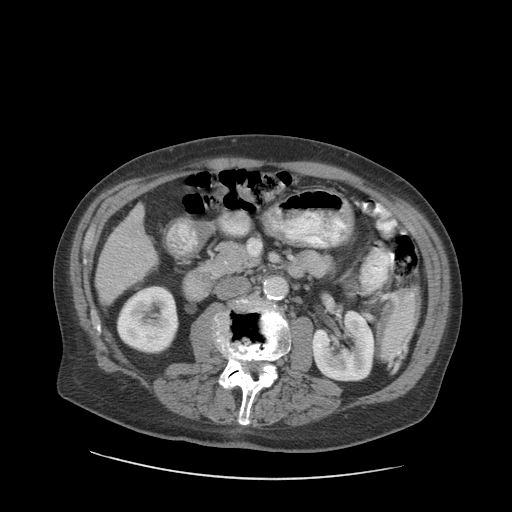
Contrast-enhanced abdominal CT (liver protocol), one axial slice; 140 kVp; soft-tissue window (W 400 / L 40 HU); 2.5 mm slice thickness; 512 × 512 image matrix, field of view 420 × 420 mm. From the clinical record (not read from this slice): diagnosis: hepatocellular carcinoma (patient treated with transarterial chemoembolisation; whether this scan precedes or follows treatment is not stated here); TNM stage (as recorded): Stage-I; Child-Pugh class: A; tumour differentiation: moderately differentiated; tumour nodularity: uninodular.
Structures marked on this image (semi-automatic segmentation, software-assisted and operator-edited):
- liver parenchyma outside the tumour (the mass and vessels are separate outlines, so this box may not span the whole liver): bounding box (x1, y1, x2, y2) in pixels: (96, 204, 156, 306)
- liver vessels: (120, 245, 132, 288)